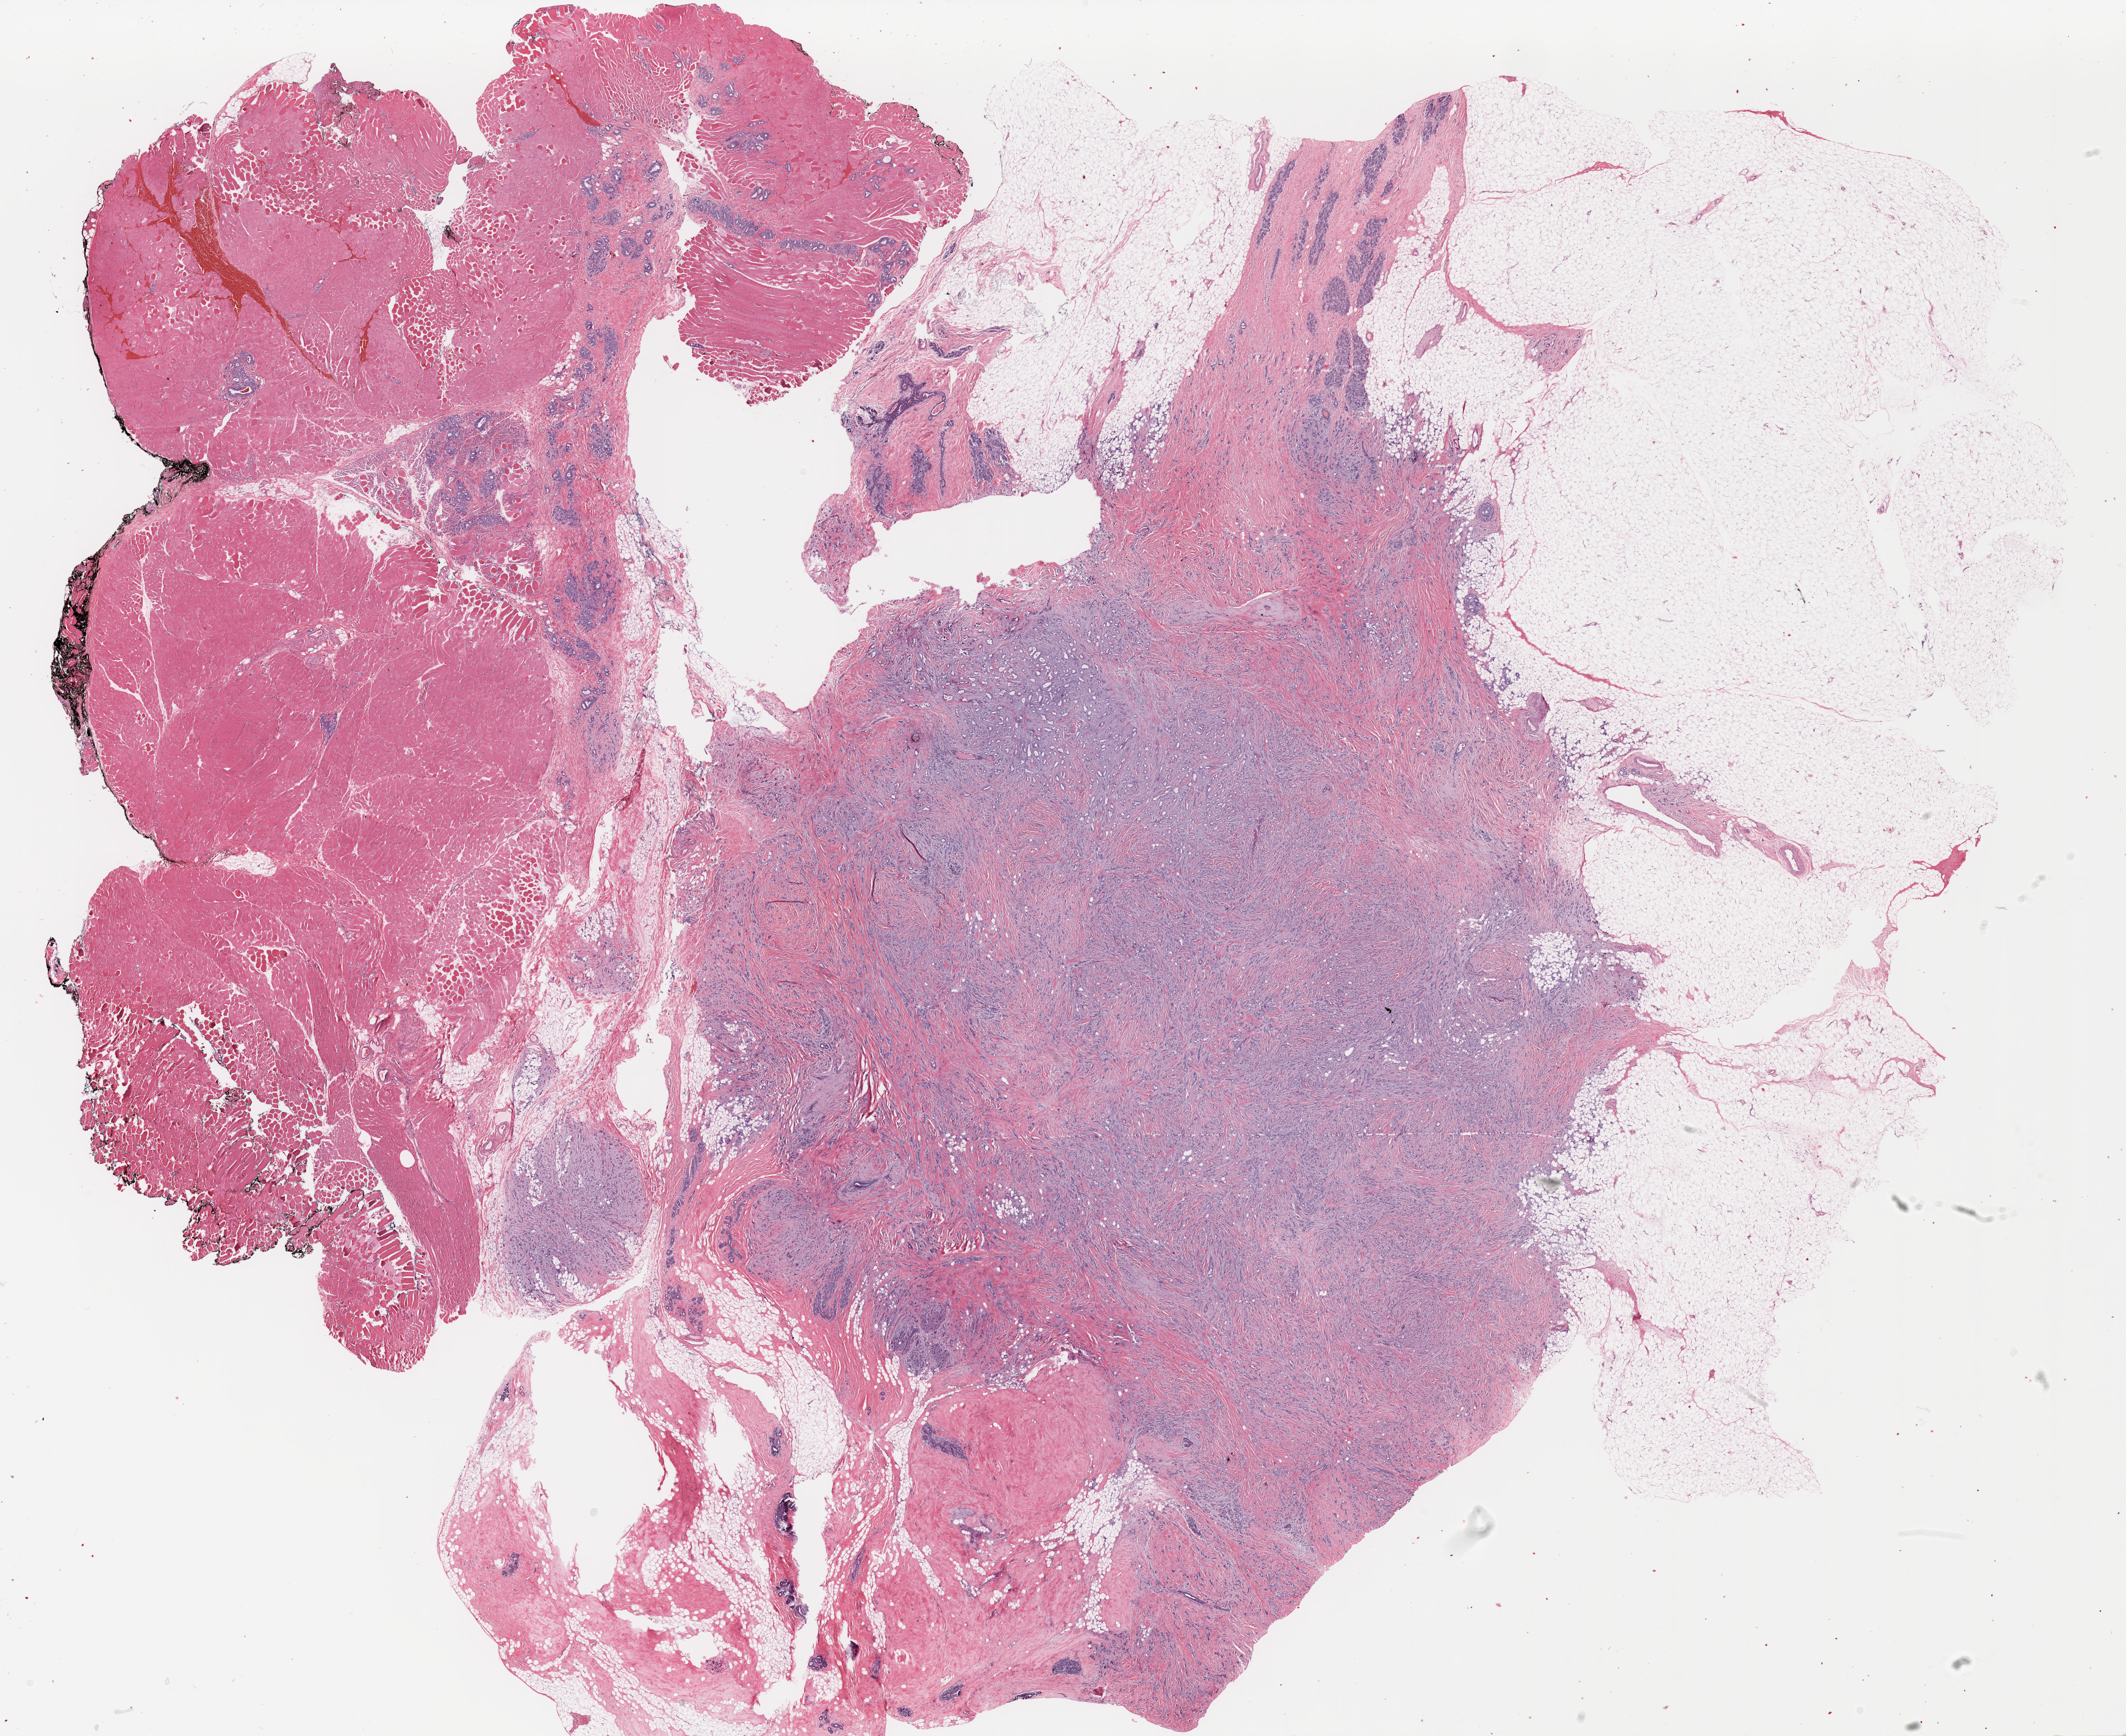
H&E whole-slide image — a low-resolution overview of the entire scanned area, about 27.8 x 22.7 mm, FFPE section, sample: primary tumour, breast. Female patient; age at initial diagnosis 48 years.
• AJCC pathologic stage: IV
• laterality: right
• lymph nodes positive (case pathology): 2 of 2 examined
• diagnosis: Infiltrating duct mixed with other types of carcinoma